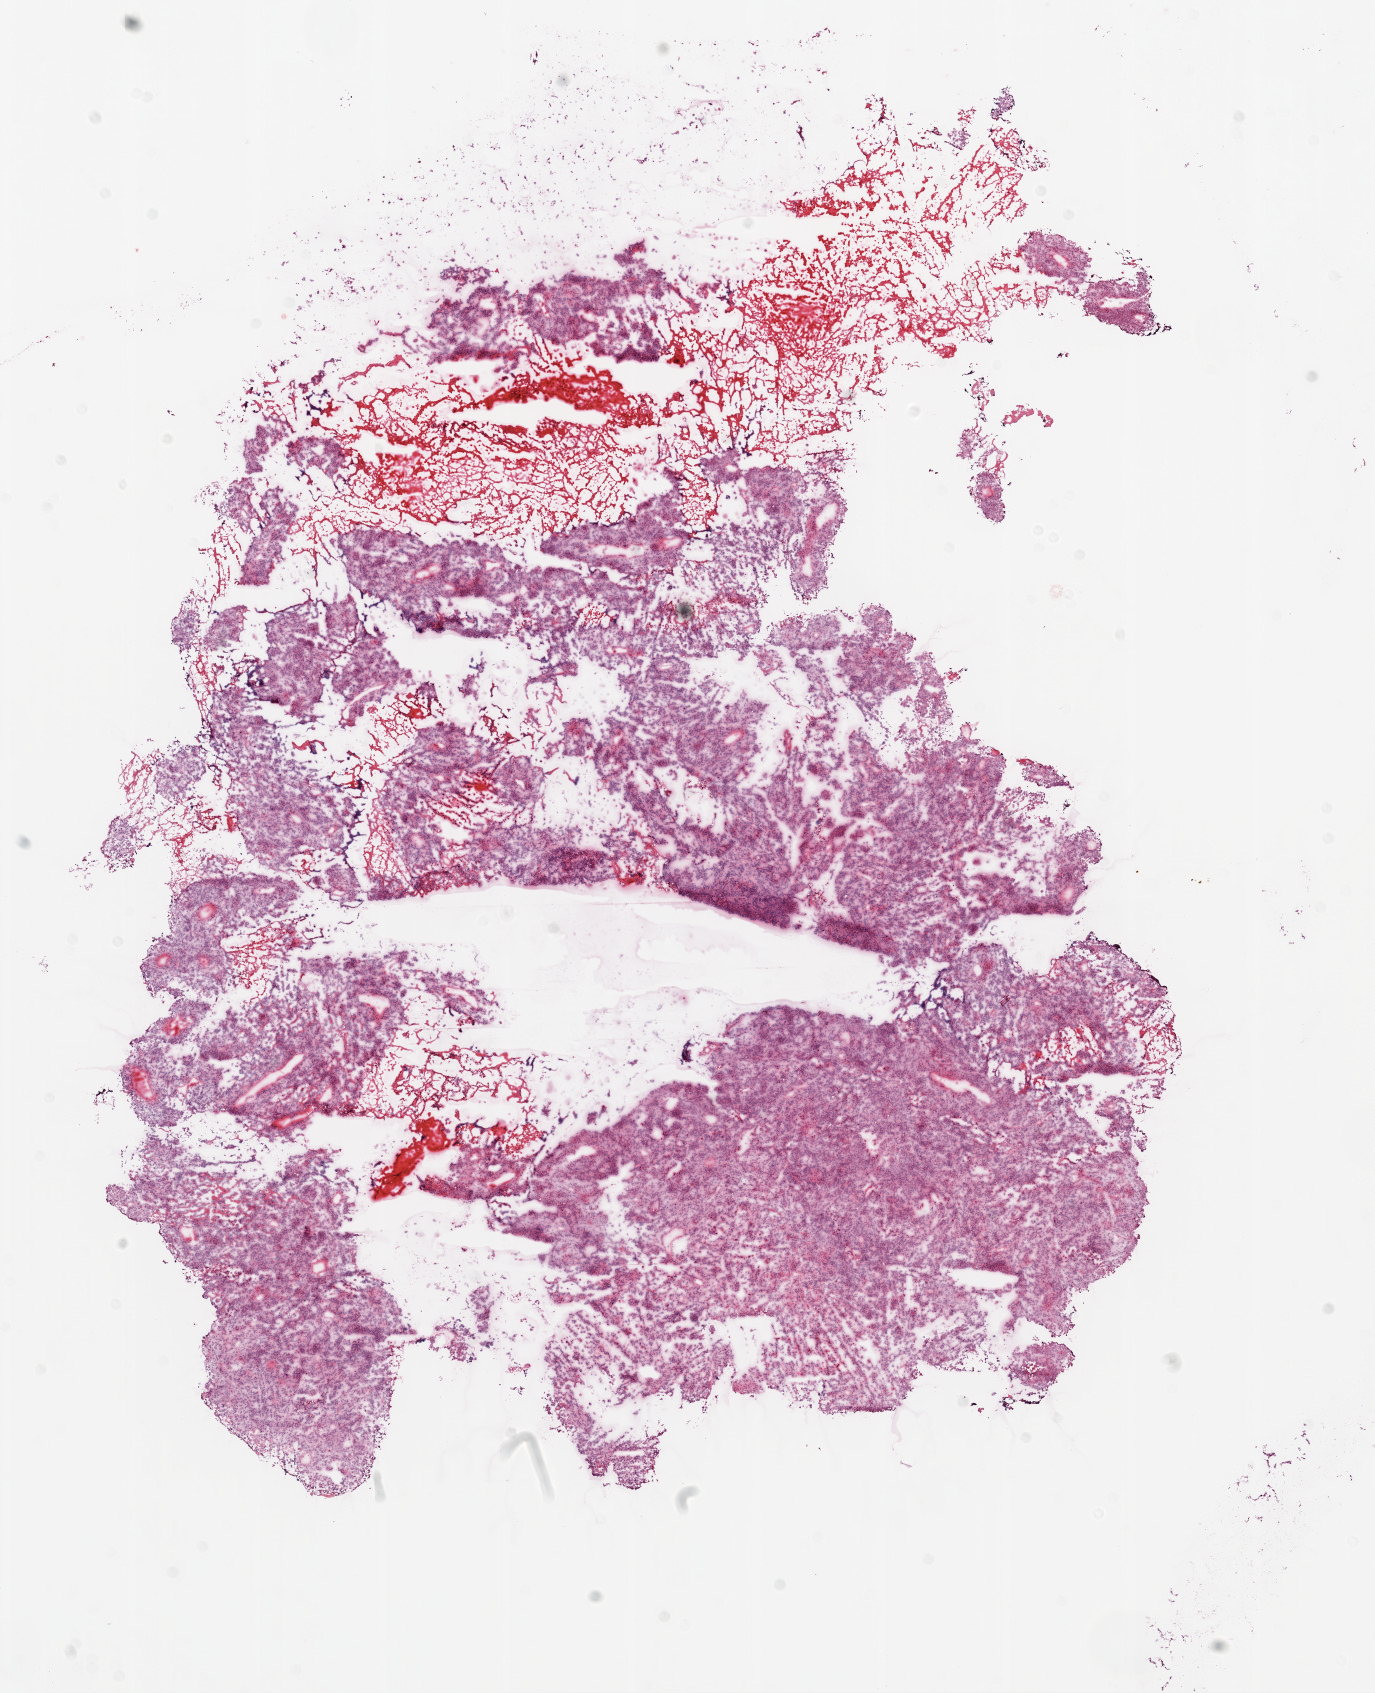
Digitized H&E tissue section (whole slide), low-resolution overview of the scanned area, about 11.0 x 13.6 mm. Frozen section from the top of the tissue portion. Primary tumour sample from the ovary. Female patient; age at initial diagnosis 81 years. Histologic grade: G3 (poorly differentiated). Slide review estimates, as recorded: tumour cells 90%, tumour nuclei 90%, normal cells 0%, stromal cells 10%, necrosis 0%. Inflammatory infiltration, as recorded: lymphocyte infiltration 0%, monocyte infiltration 0%, neutrophil infiltration 0%.
FIGO stage: IIIC. Diagnosis: Serous cystadenocarcinoma, NOS.